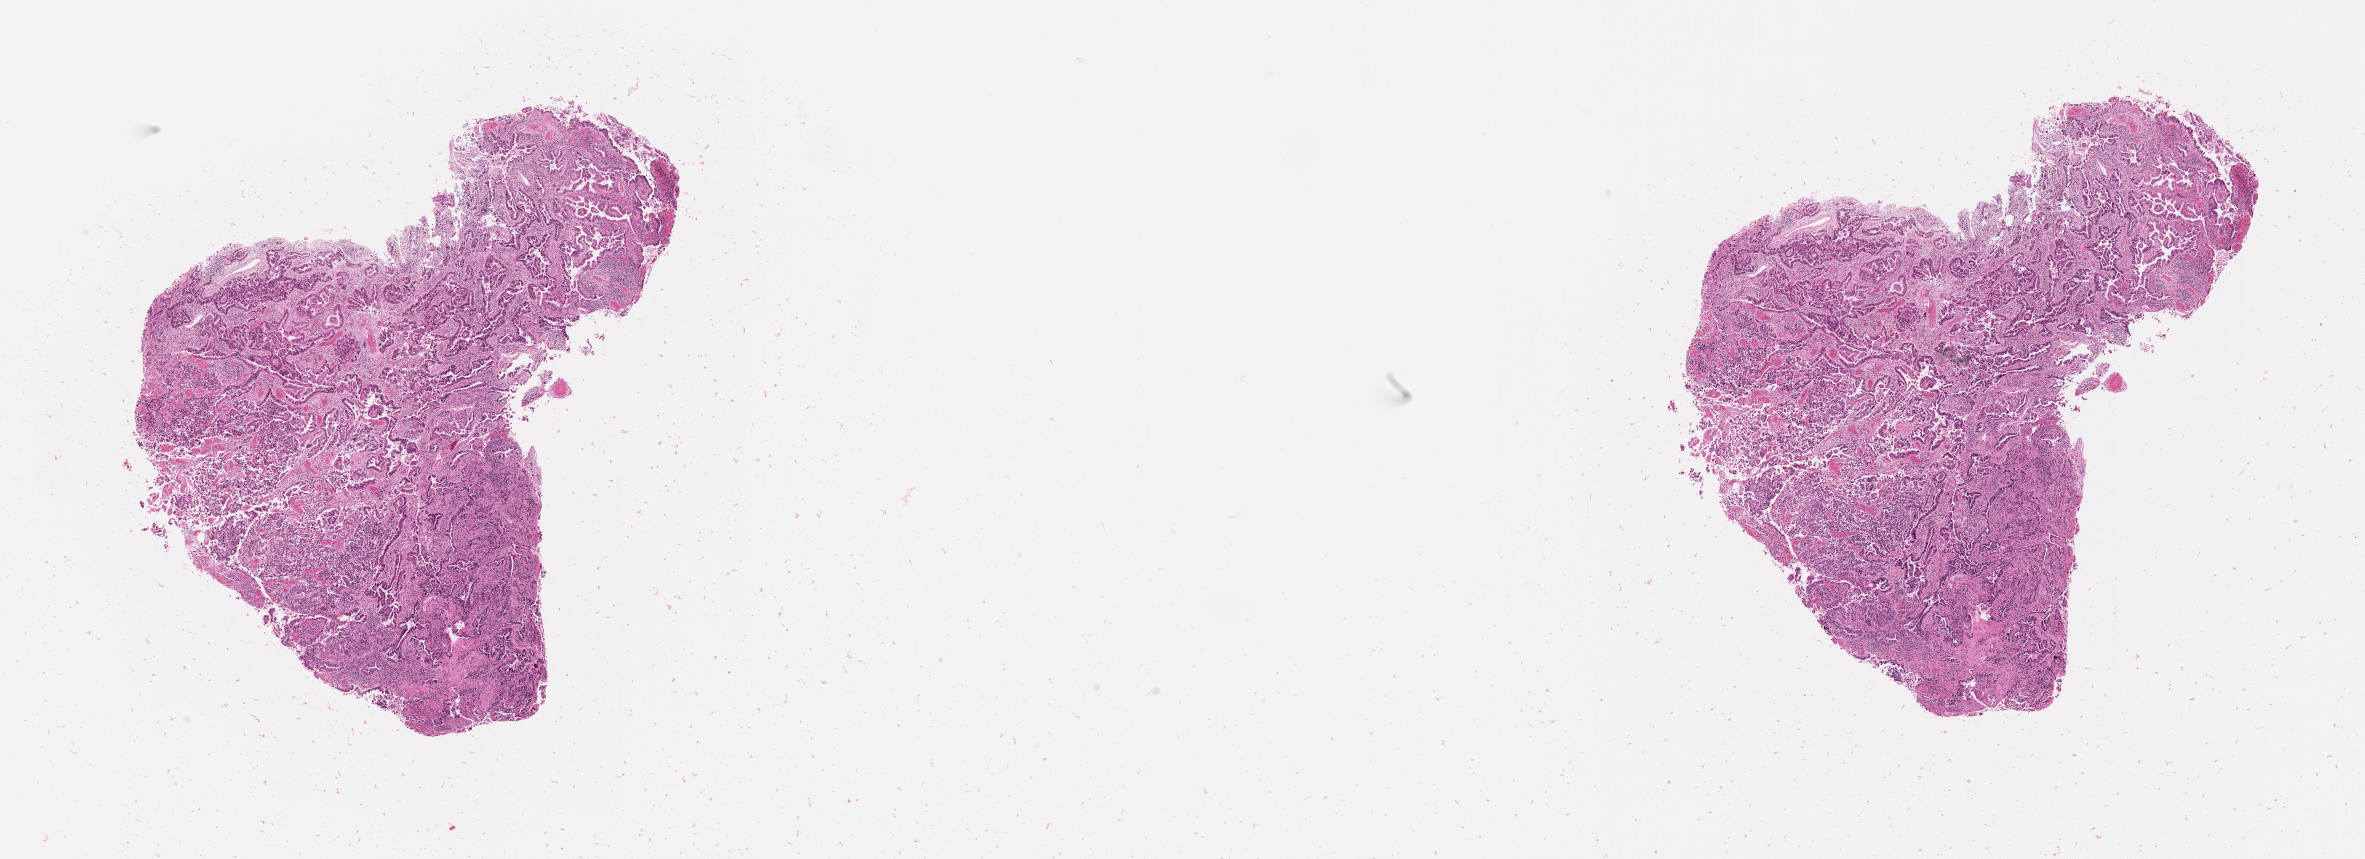
Whole-slide histology image, Hematoxylin and eosin (H&E) stained — a low-resolution overview of the entire scanned area, about 19.0 x 6.9 mm, tumour tissue sample, uterus. Female, 64 y/o. Histologic grade: G3 (poorly differentiated).
- AJCC pathologic stage: IIIC2
- diagnosis: Endometrioid adenocarcinoma, NOS